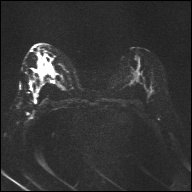
Breast MRI, one axial slice; slice 16 of 32 in the series (ordered by position); diffusion-weighted series; image 2 of 4 stored at this slice position (different b-values; order by instance number); 1.5 T; 4 mm slice thickness; 192 × 192 image matrix, field of view 360 × 360 mm. Female patient.
Outlined on this slice (outlined manually by an expert reader):
- tumour on diffusion-weighted imaging: bounding box [x1, y1, x2, y2] px = [38, 61, 42, 68]